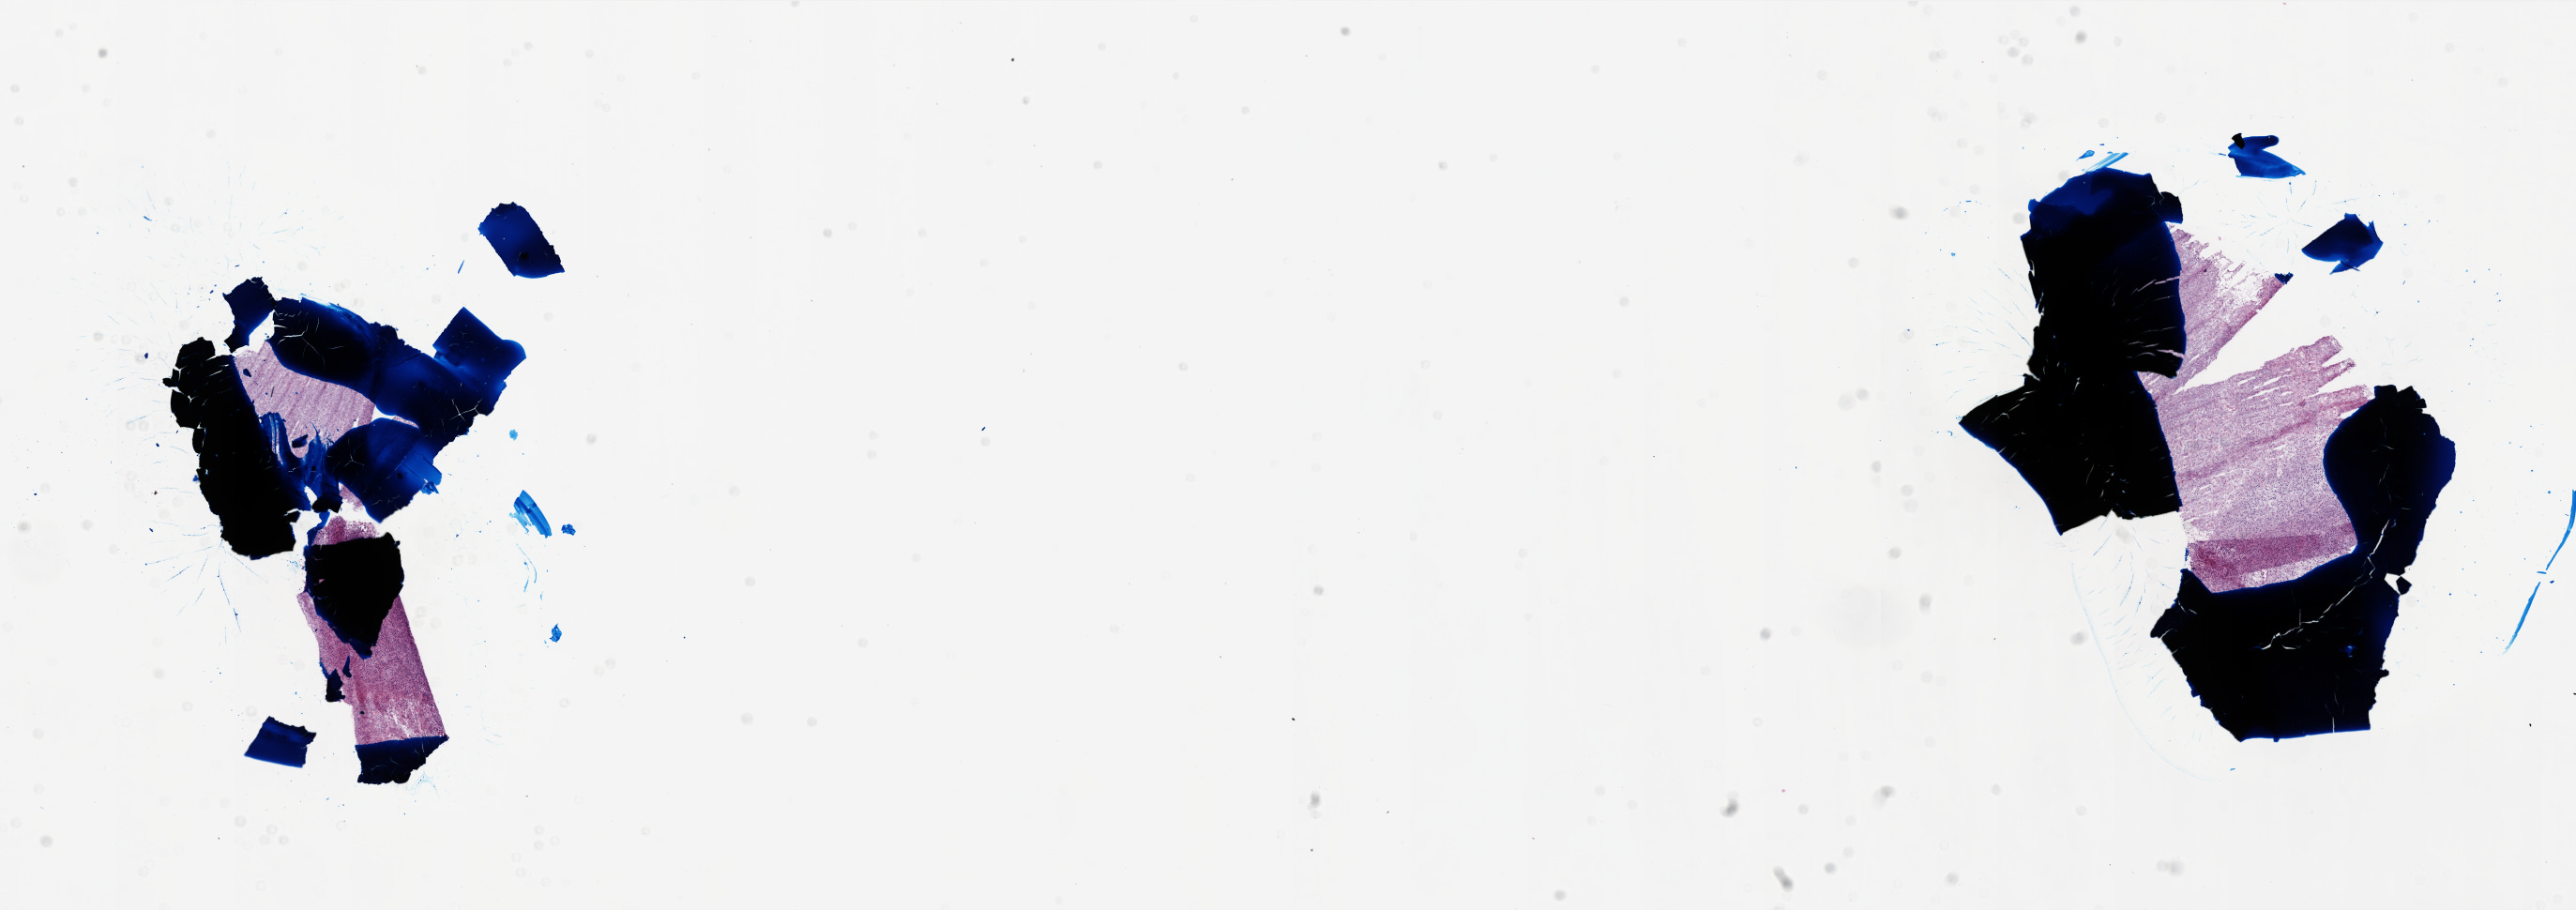
H&E whole-slide image, a low-resolution overview of the entire scanned area, about 22.0 x 7.8 mm, frozen section from the top of the tissue portion, sample: primary tumour, brain. Male patient; age at initial diagnosis 47 years. Pathologist review of this section (percent, as recorded): tumour cells 50%, tumour nuclei 95%, normal cells 0%, stromal cells 5%, necrosis 45%.
* histologic diagnosis: Glioblastoma